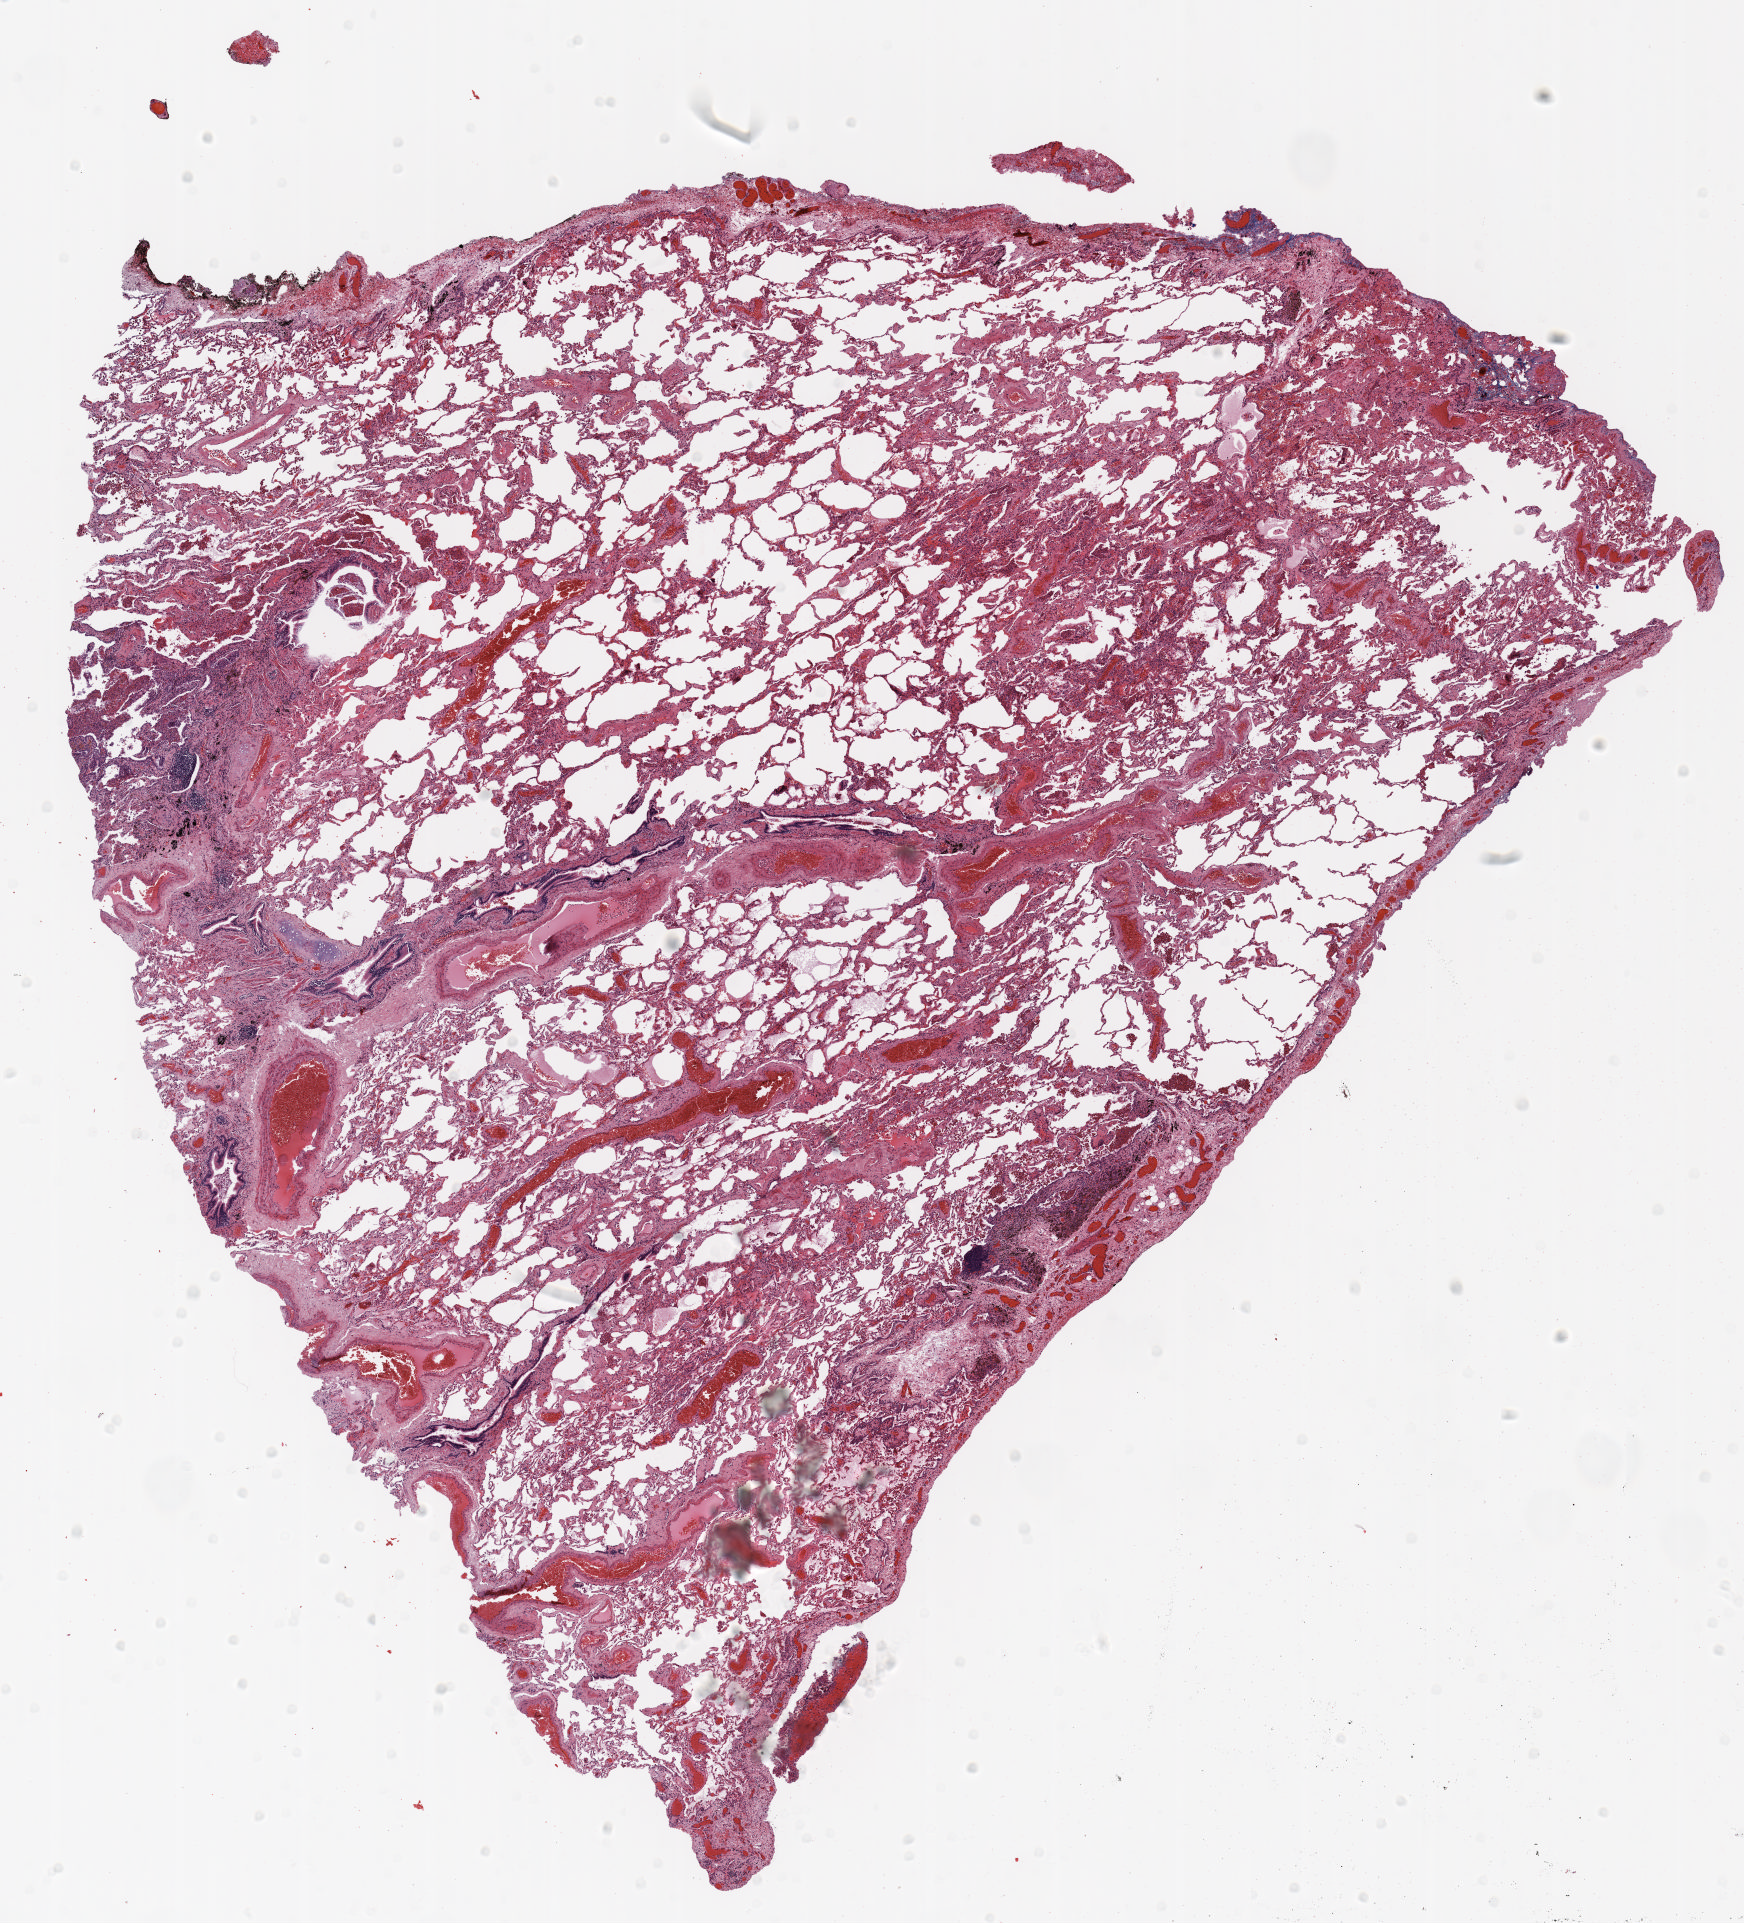
H&E whole-slide image, a low-resolution overview of the entire scanned area, about 14.0 x 15.5 mm. Formalin-fixed paraffin-embedded (FFPE) section. Lung. Male patient, aged 65 at enrolment. Current smoker at enrolment. Grade: poorly differentiated (G3).
Stage (AJCC 6th edition): IA. Participant's lung-cancer diagnosis: Squamous cell carcinoma, NOS (ICD-O-3 8070/3). Primary tumour location (clinical record): left upper lobe. Tumour size (pathology): 18 mm.